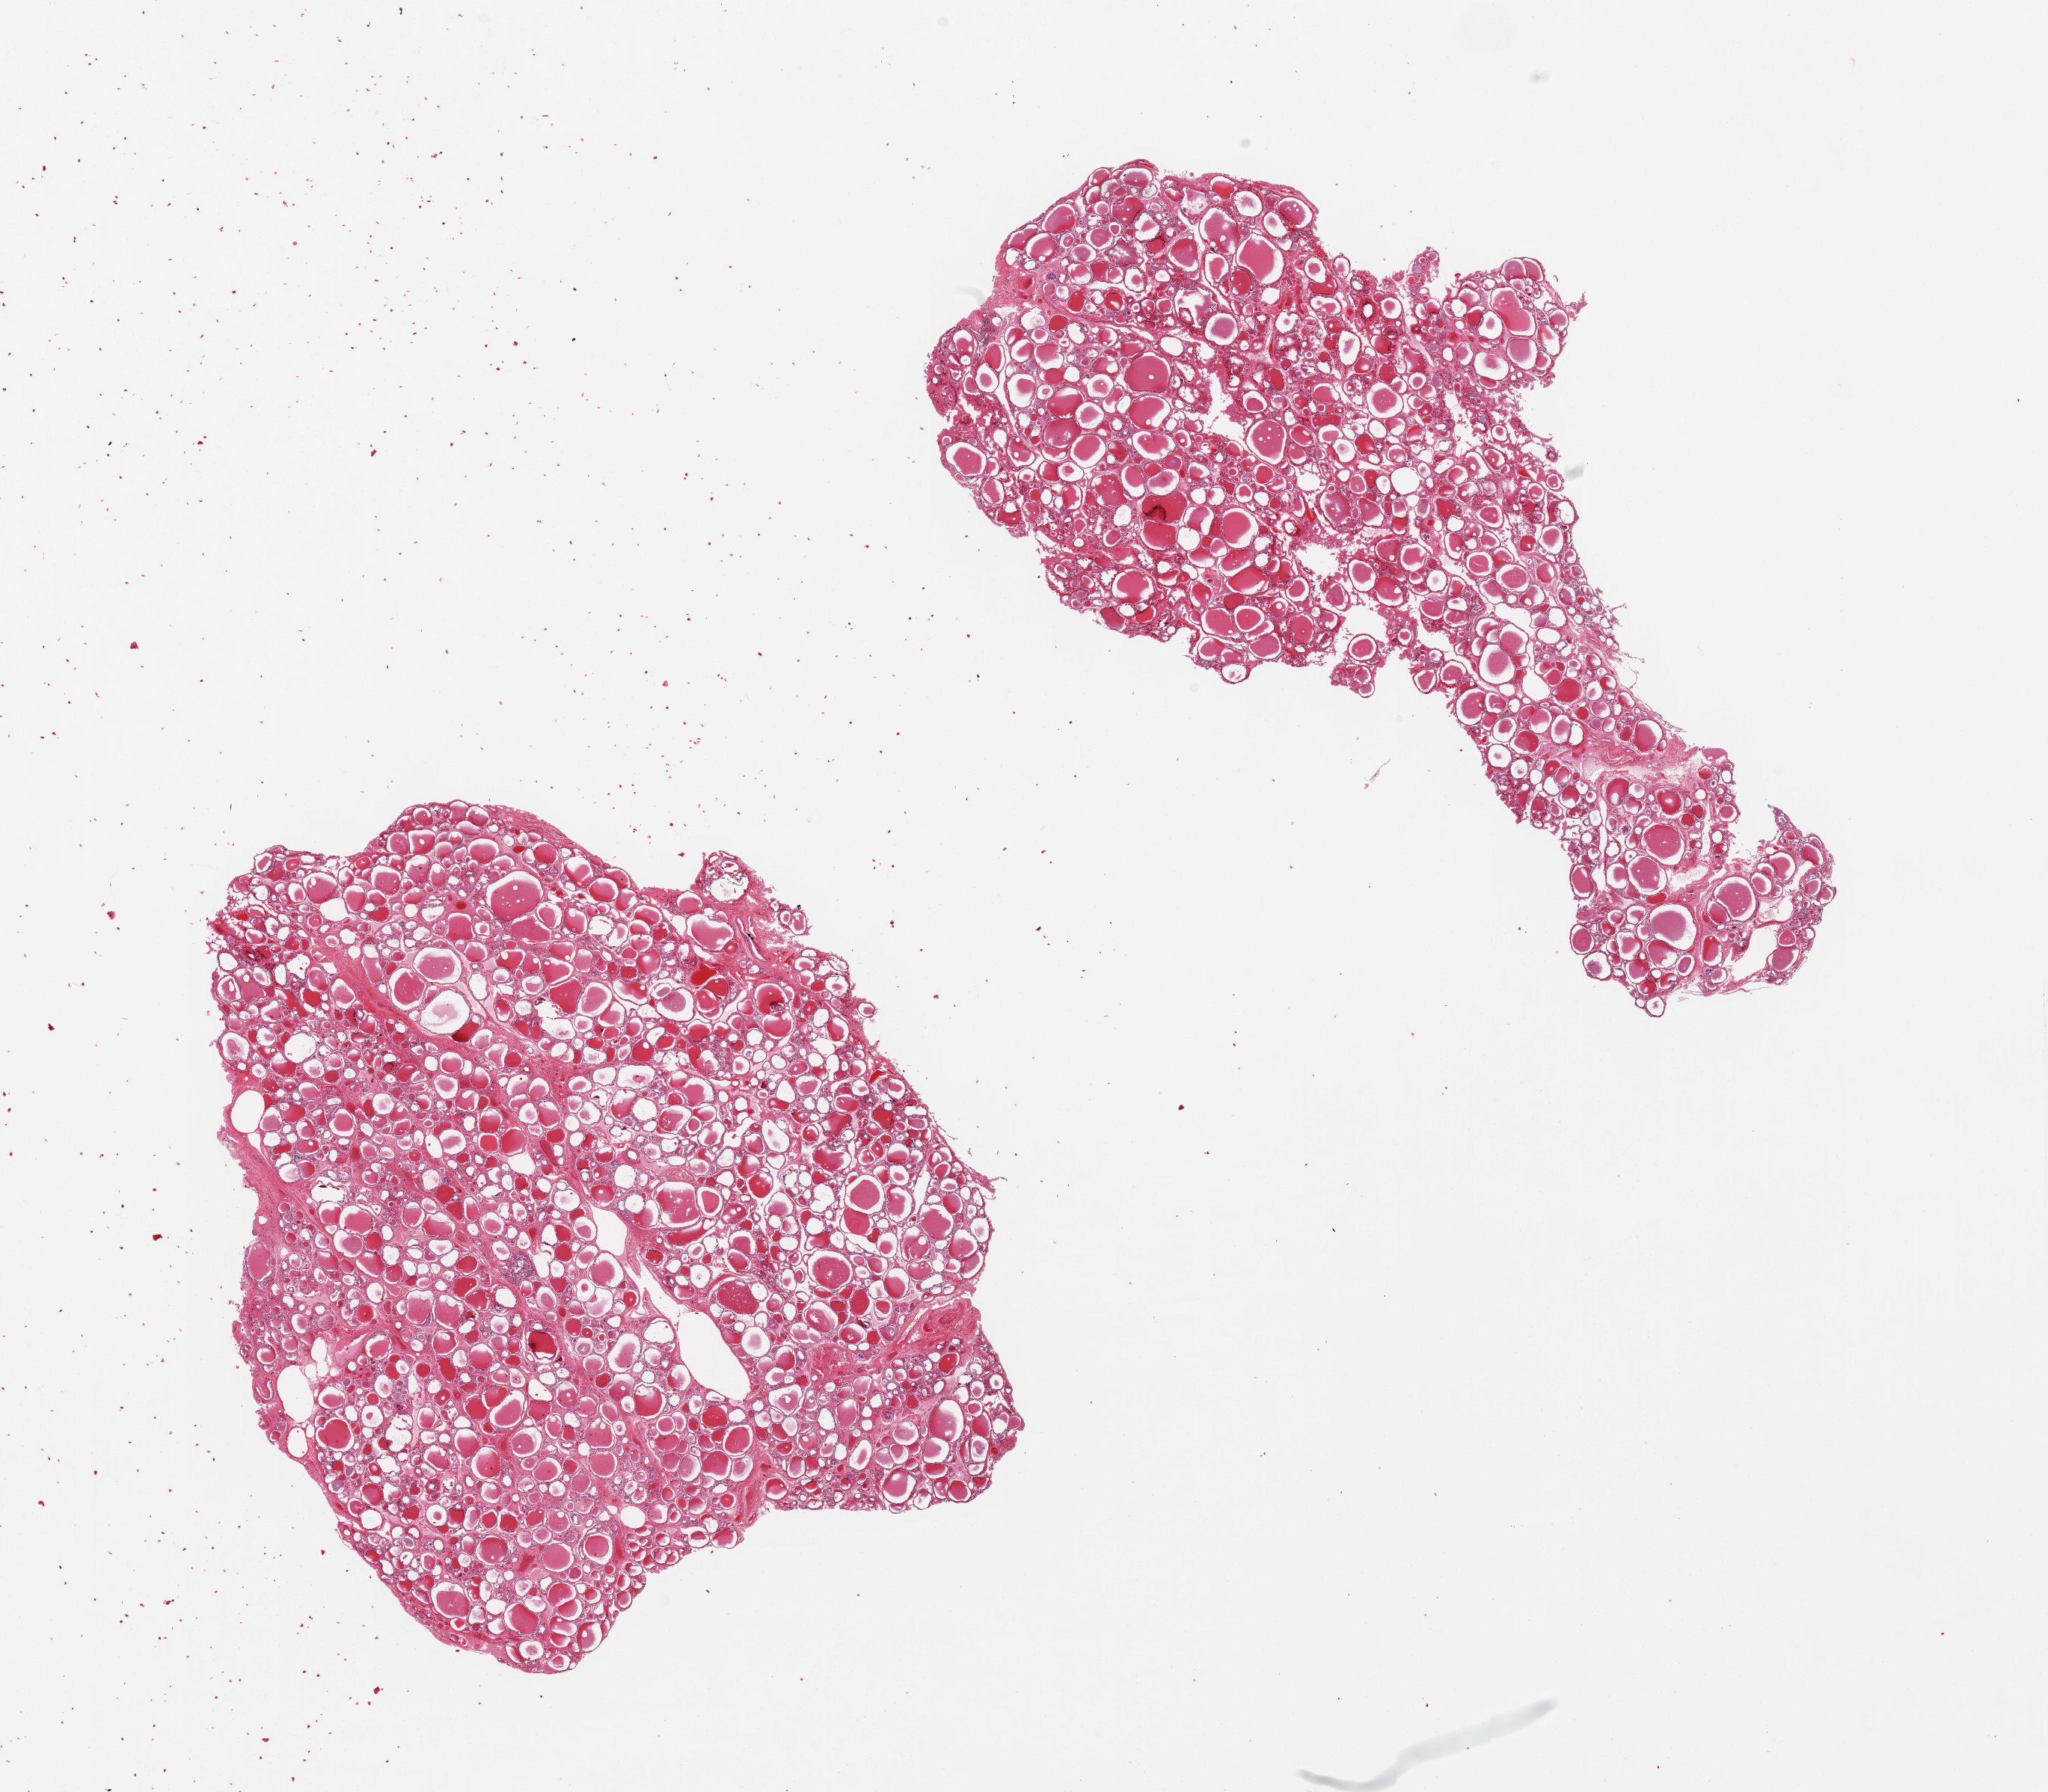
Digitized hematoxylin and eosin (H&E)-stained section, shown as a low-resolution overview of the whole scanned area (about 21.7 x 19.0 mm, slide scanned at 20x); PAXgene-fixed, paraffin-embedded tissue; target tissue: thyroid; donor tissue sample. Donor: male.
• reviewer comment on this tissue sample: 2 pieces